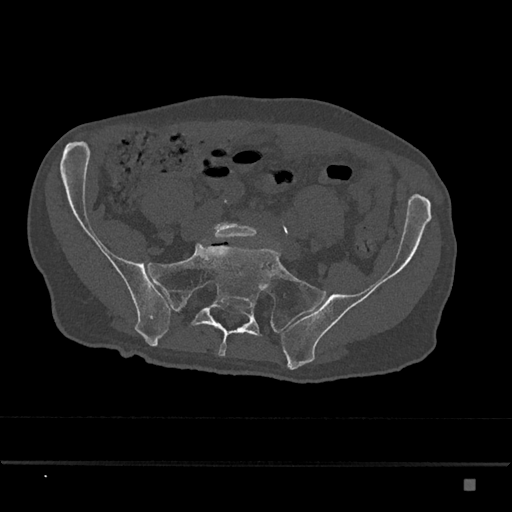
CT including the spine, one axial slice; position 211 of 797 along the scan axis; reconstruction kernel Br40s/3; bone window (W 1800 / L 400 HU); 0.5 mm slice thickness; 512 × 512 image matrix. Patient: male, 72 years. Case-level facts recorded for this patient, not image findings: primary cancer: prostate.
Annotated regions visible in this slice (semi-automatic segmentation, software-assisted and operator-edited):
- L5 vertebra: box from (x=212, y=223) to (x=257, y=240) px